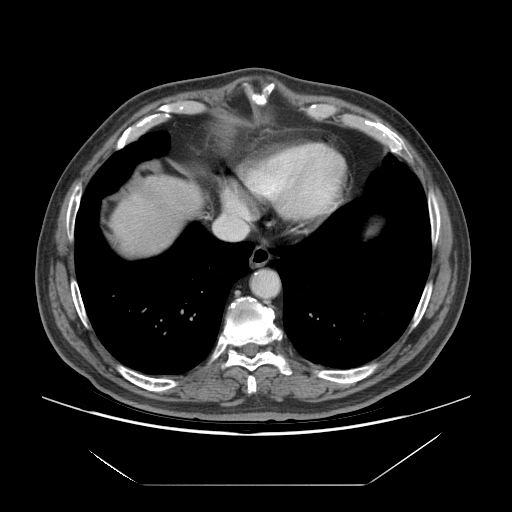
Contrast-enhanced abdominal CT (liver protocol), one axial slice. Position 66 of 75 along the scan axis. Reconstruction kernel STANDARD. Soft-tissue window (W 400 / L 40 HU). 2.5 mm slice thickness. 512 × 512 image matrix, field of view 420 × 420 mm. From the clinical record (not read from this slice): diagnosis: hepatocellular carcinoma (patient treated with transarterial chemoembolisation; whether this scan precedes or follows treatment is not stated here); TNM stage (as recorded): Stage-I; Child-Pugh class: A; tumour differentiation: well differentiated; tumour nodularity: uninodular.
Annotated regions visible in this slice (semi-automatic segmentation, software-assisted and operator-edited):
- liver parenchyma outside the tumour (the mass and vessels are separate outlines, so this box may not span the whole liver): box from (x=112, y=176) to (x=202, y=254) px